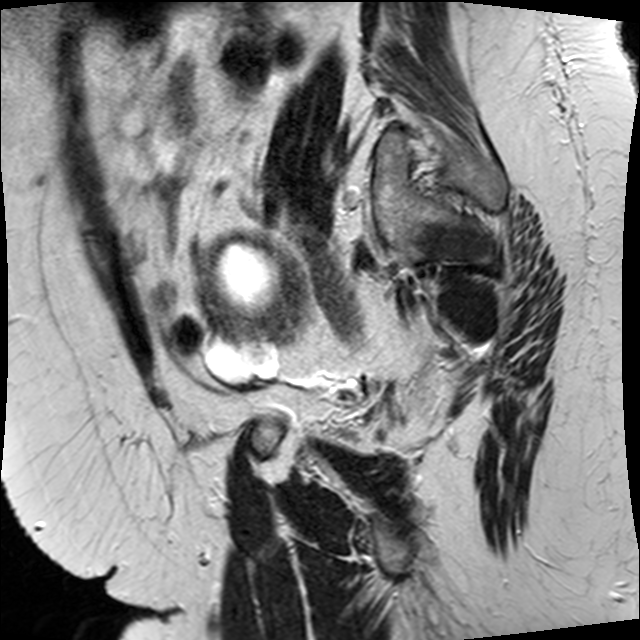
Pelvic MRI for cervical cancer, one sagittal slice. Slice 27 of 34 in the series (ordered by position). T2-weighted. 1.5 T. TE 89 ms, TR 3320 ms. 4 mm slice thickness. 640 × 640 image matrix, field of view 260 × 260 mm. Female patient, age 50 years.
Structures marked on this image (manually delineated by an expert):
- uterus and cervix: box from (x=197, y=229) to (x=308, y=342) px